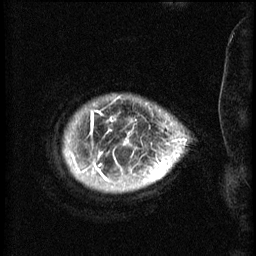
Breast MRI (dynamic contrast-enhanced), one sagittal slice. Position 56 of 60 along the scan axis. 3 images stored at this slice position (order not interpretable as contrast timing). 1.5 T. TE 4.2 ms, TR 8.2 ms. 256 × 256 image matrix, field of view 200 × 200 mm. Female patient, age 50 years.
Annotated regions visible in this slice (semi-automatically segmented with operator editing):
- analysis volume of interest (the breast-tissue region the enhancement analysis was run in; not a lesion): bounding box (x1, y1, x2, y2) in pixels: (66, 102, 169, 191)
- tumour enhancement mask (voxels above the 70 % enhancement threshold inside the analysis volume of interest): (72, 112, 165, 181)